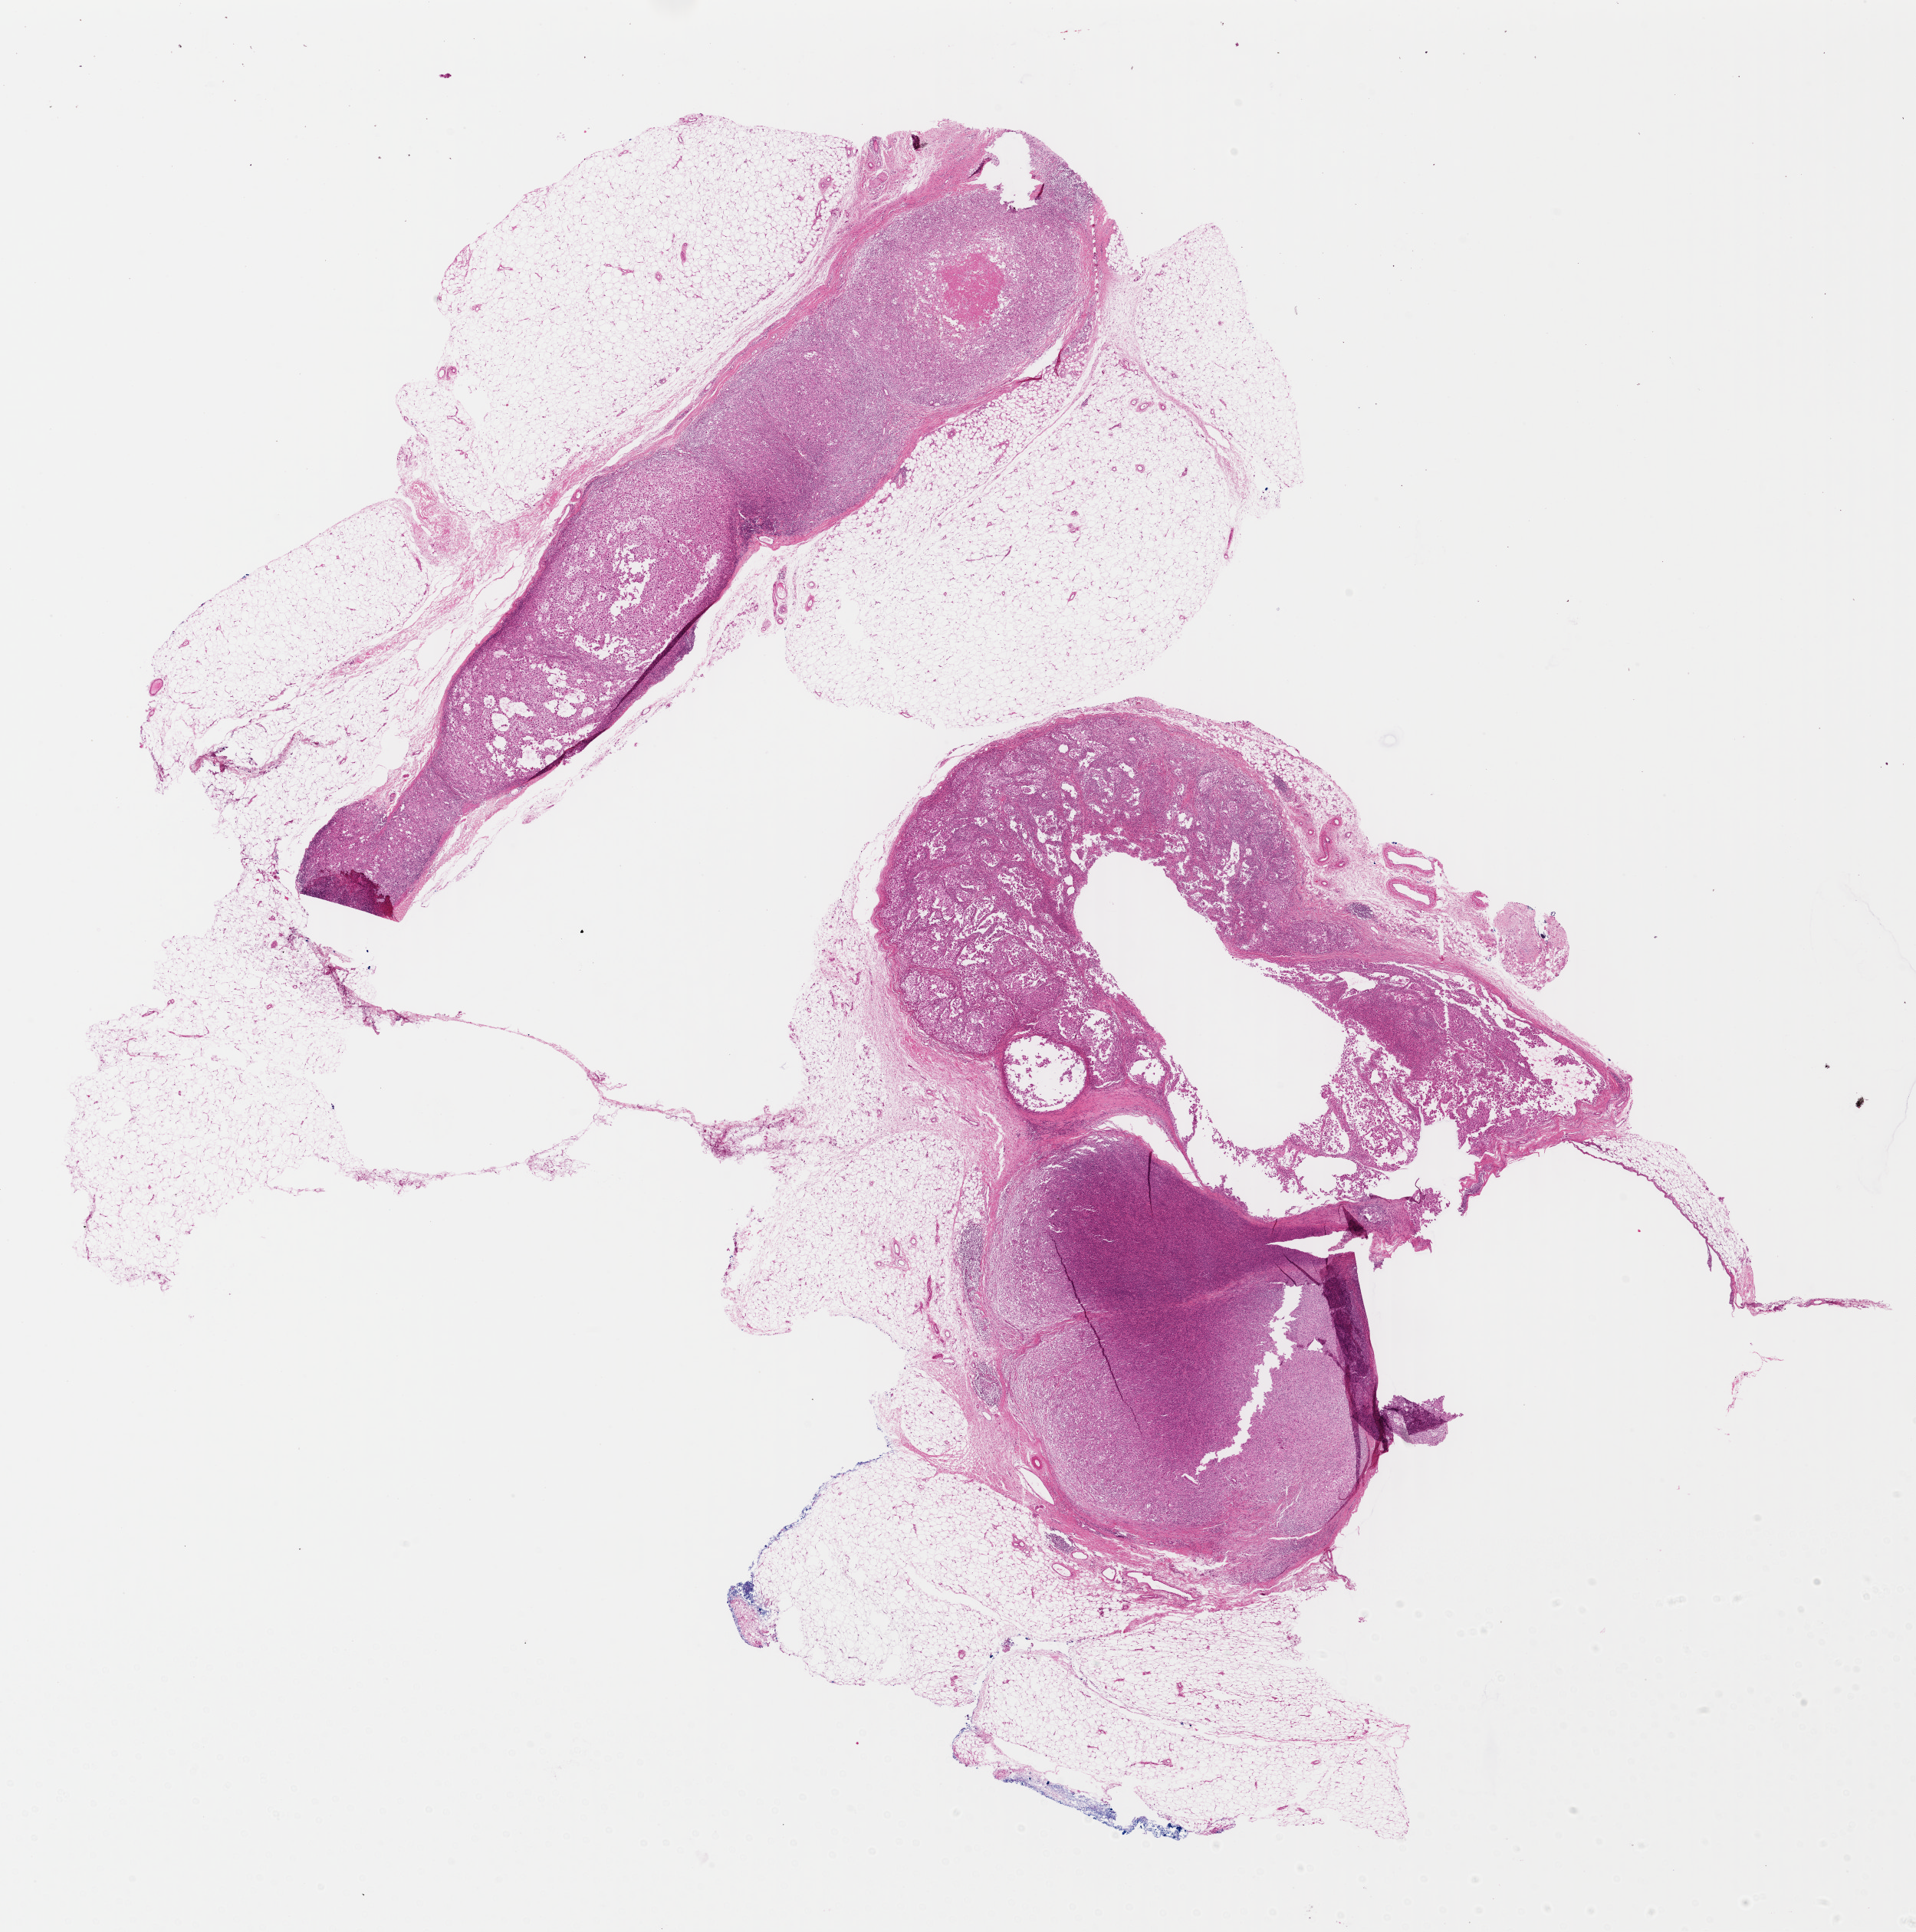
Hematoxylin and eosin (H&E) stained whole-slide image — a low-resolution overview of the entire scanned area, about 19.6 x 19.8 mm, FFPE section, primary tumour sample from the skin. Female, age 54 years at initial diagnosis.
- diagnosis: Malignant melanoma, NOS